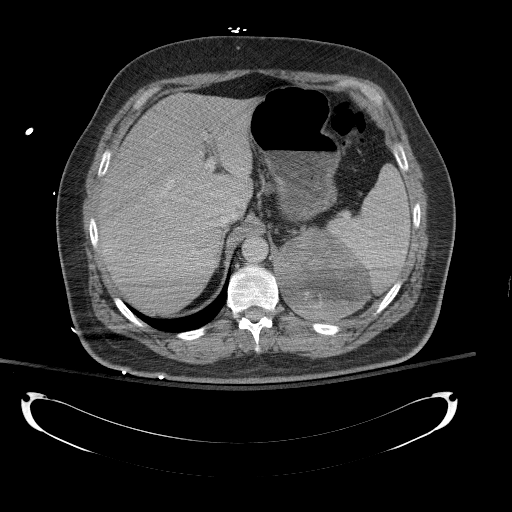
Contrast-enhanced abdominal CT, one axial slice; position 93 of 154 along the scan axis; reconstruction kernel B41f; intravenous contrast given; soft-tissue window (W 400 / L 40 HU); 5 mm slice thickness; 512 × 512 image matrix. Male patient, age 43 years. From the clinical record (not read from this slice): diagnosis: adrenocortical carcinoma; tumour side: left adrenal.
Outlined on this slice (semi-automatic segmentation, software-assisted and operator-edited):
- mass: box from (x=279, y=228) to (x=370, y=319) px